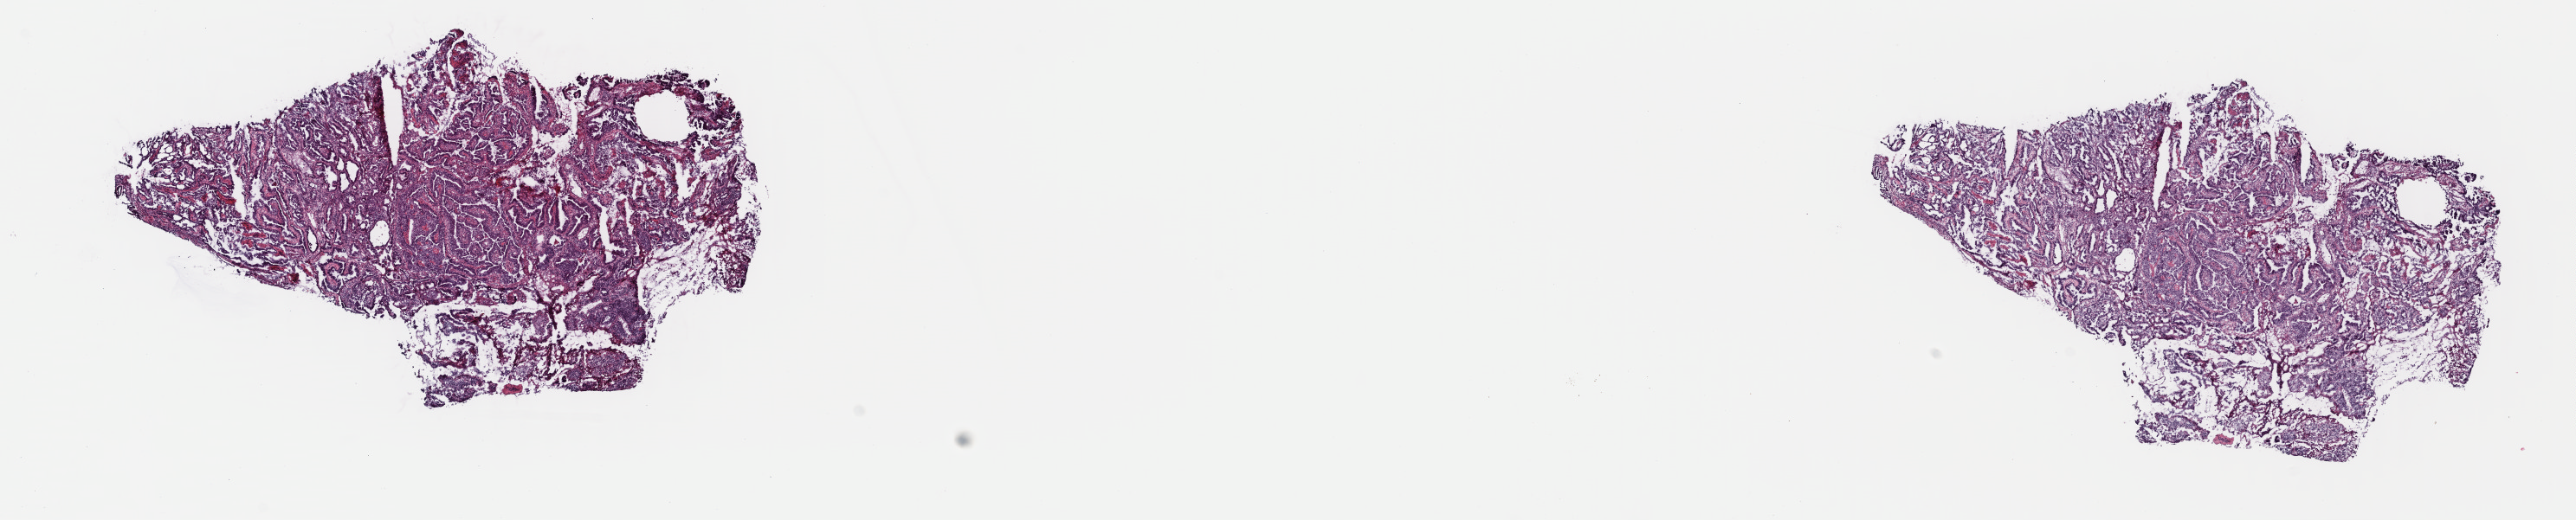
Whole-slide histology image, H&E — shown as a low-resolution overview of the whole scanned area (about 23.4 x 4.7 mm, from a 40x scan). Frozen section from the top of the tissue portion. Cervix, primary tumour sample. Female patient; age at initial diagnosis 32 years. Histologic grade: G2 (moderately differentiated). Pathologist review of this section (percent, as recorded): tumour cells 100%, tumour nuclei 75%, normal cells 0%, stromal cells 0%, necrosis 0%. Inflammatory infiltration, as recorded: lymphocyte infiltration 4%, monocyte infiltration 0%, neutrophil infiltration 0%.
FIGO stage: IB1. Diagnosis: Mucinous adenocarcinoma, endocervical type. Lymph nodes positive (case pathology): 0 of 4 examined.